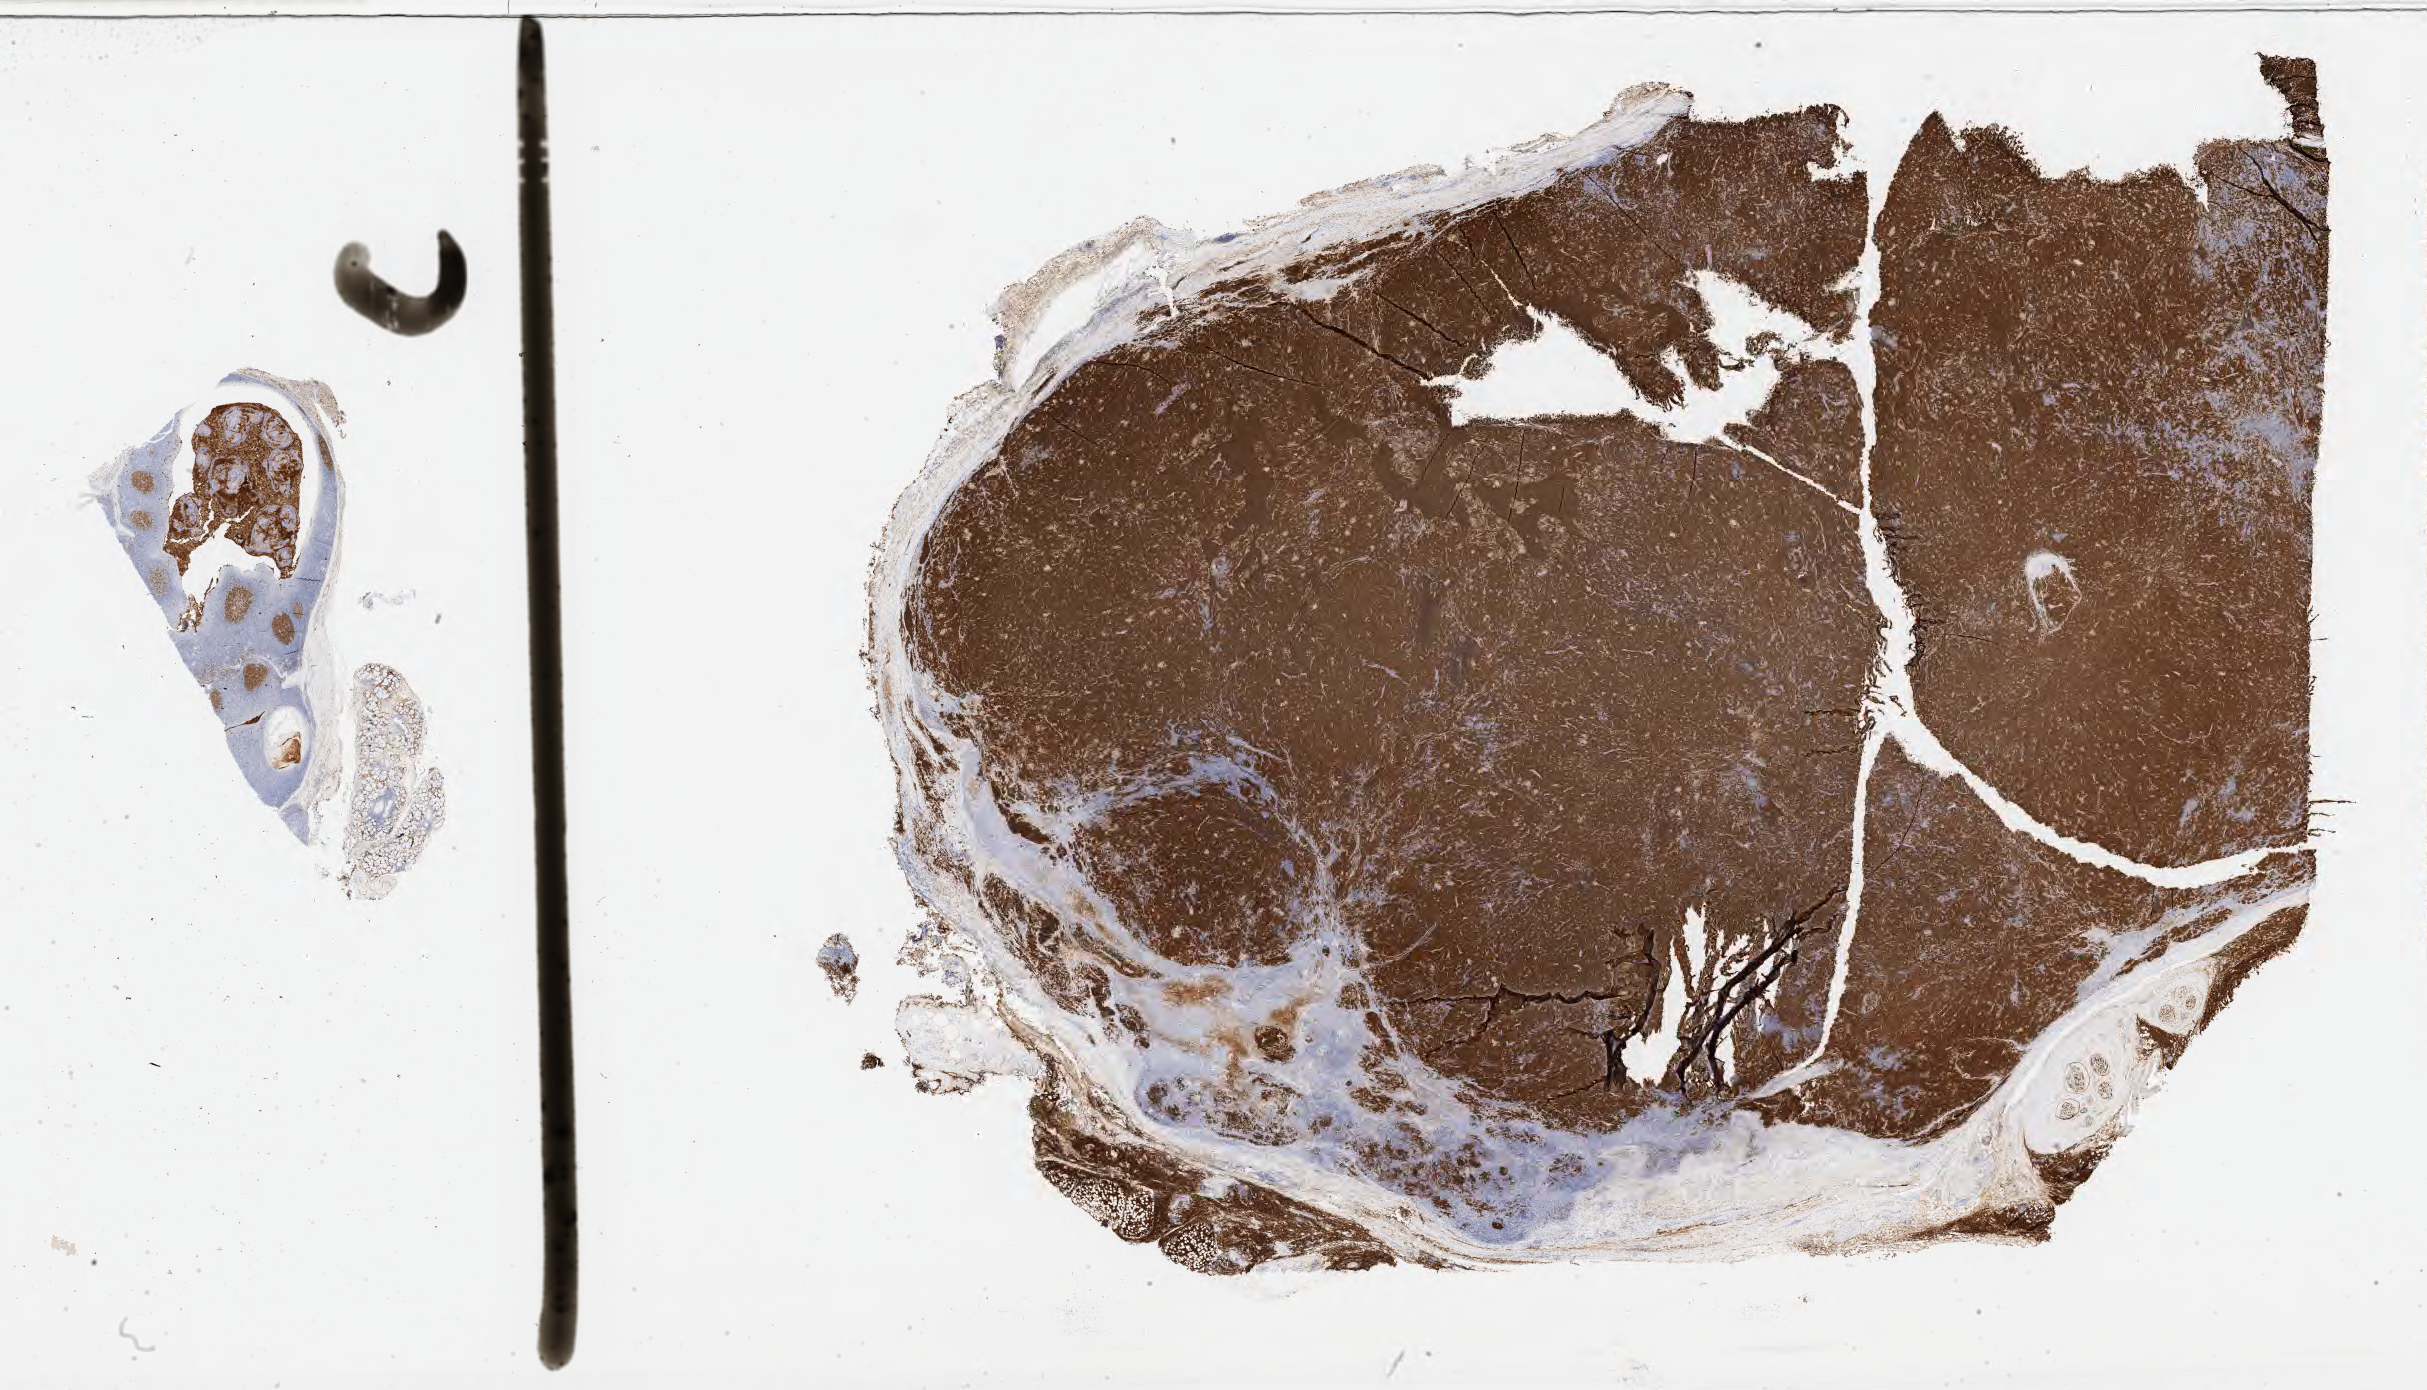
IHC for CD10, whole-slide image — a low-resolution overview of the entire scanned area, about 39.3 x 22.5 mm. Tumor tissue. Patient male; aged 30.
Histologic diagnosis: Burkitt lymphoma, NOS.